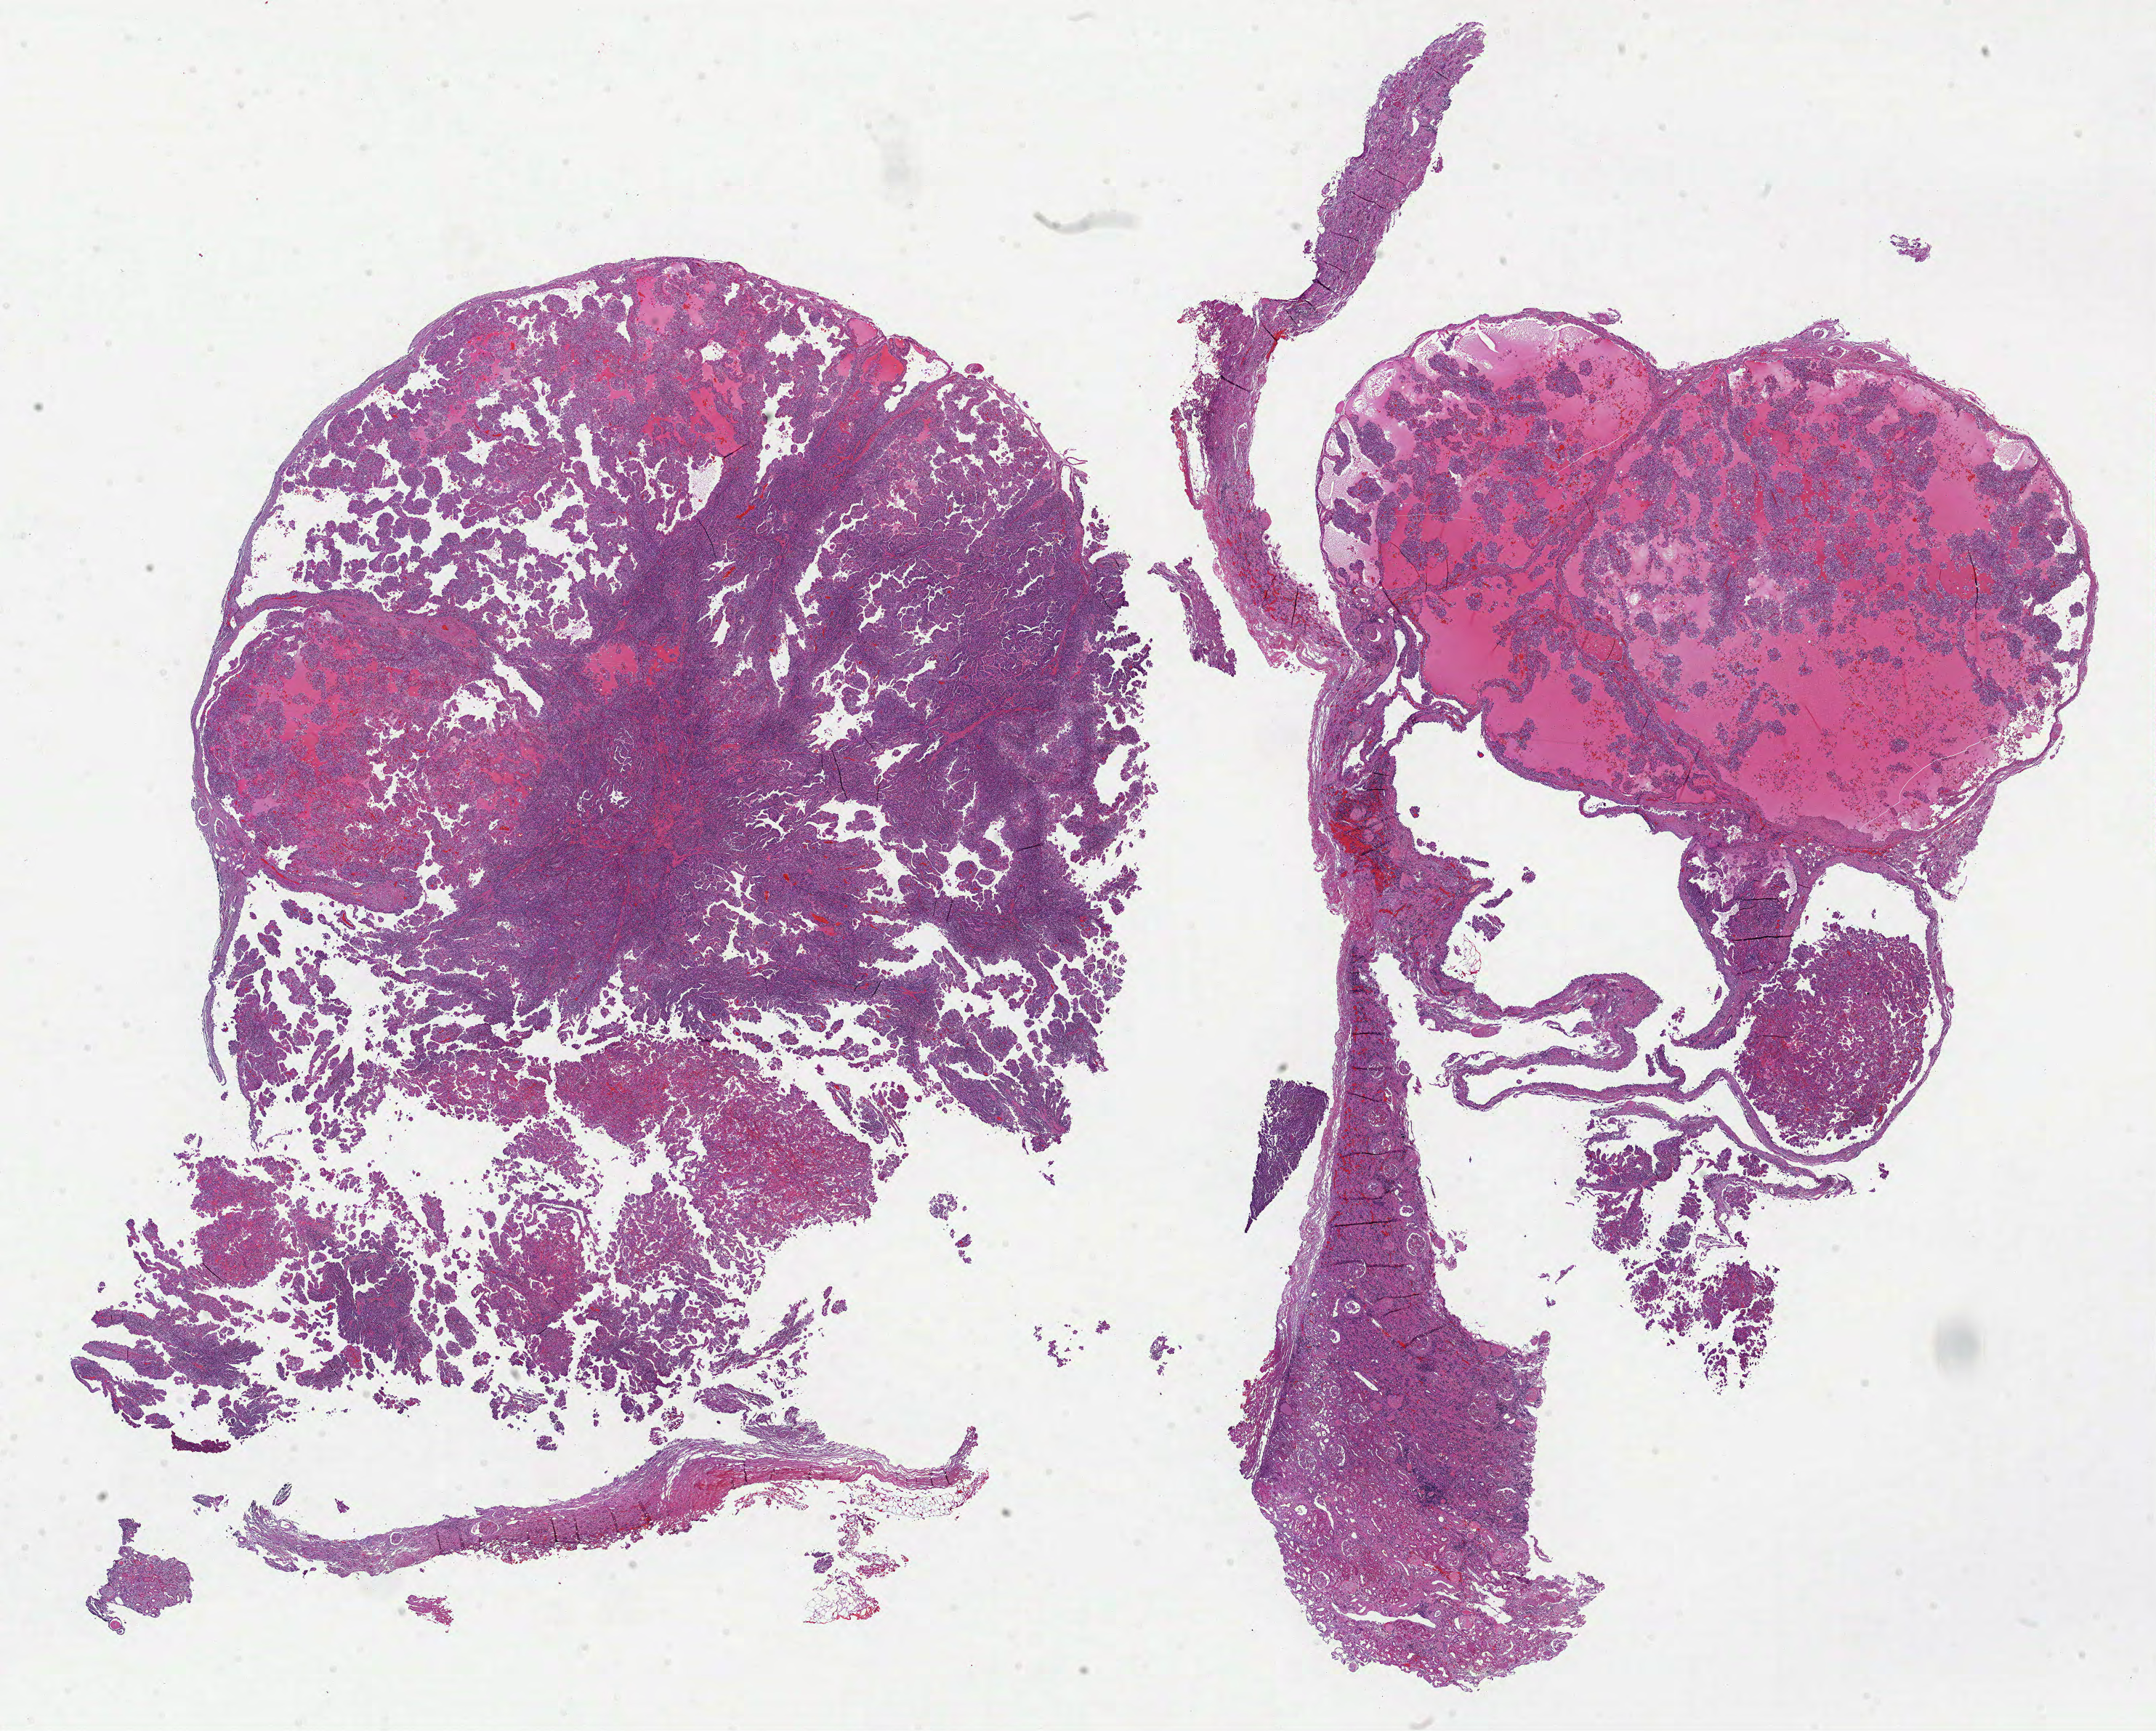
Digitized H&E tissue section (whole slide) — low-resolution overview of the scanned area, about 23.9 x 19.2 mm (from a 40x scan). FFPE section. Kidney, primary tumour sample. Patient: male, age at initial diagnosis 61 years.
- AJCC pathologic stage: I (7th edition)
- histologic diagnosis: Papillary adenocarcinoma, NOS